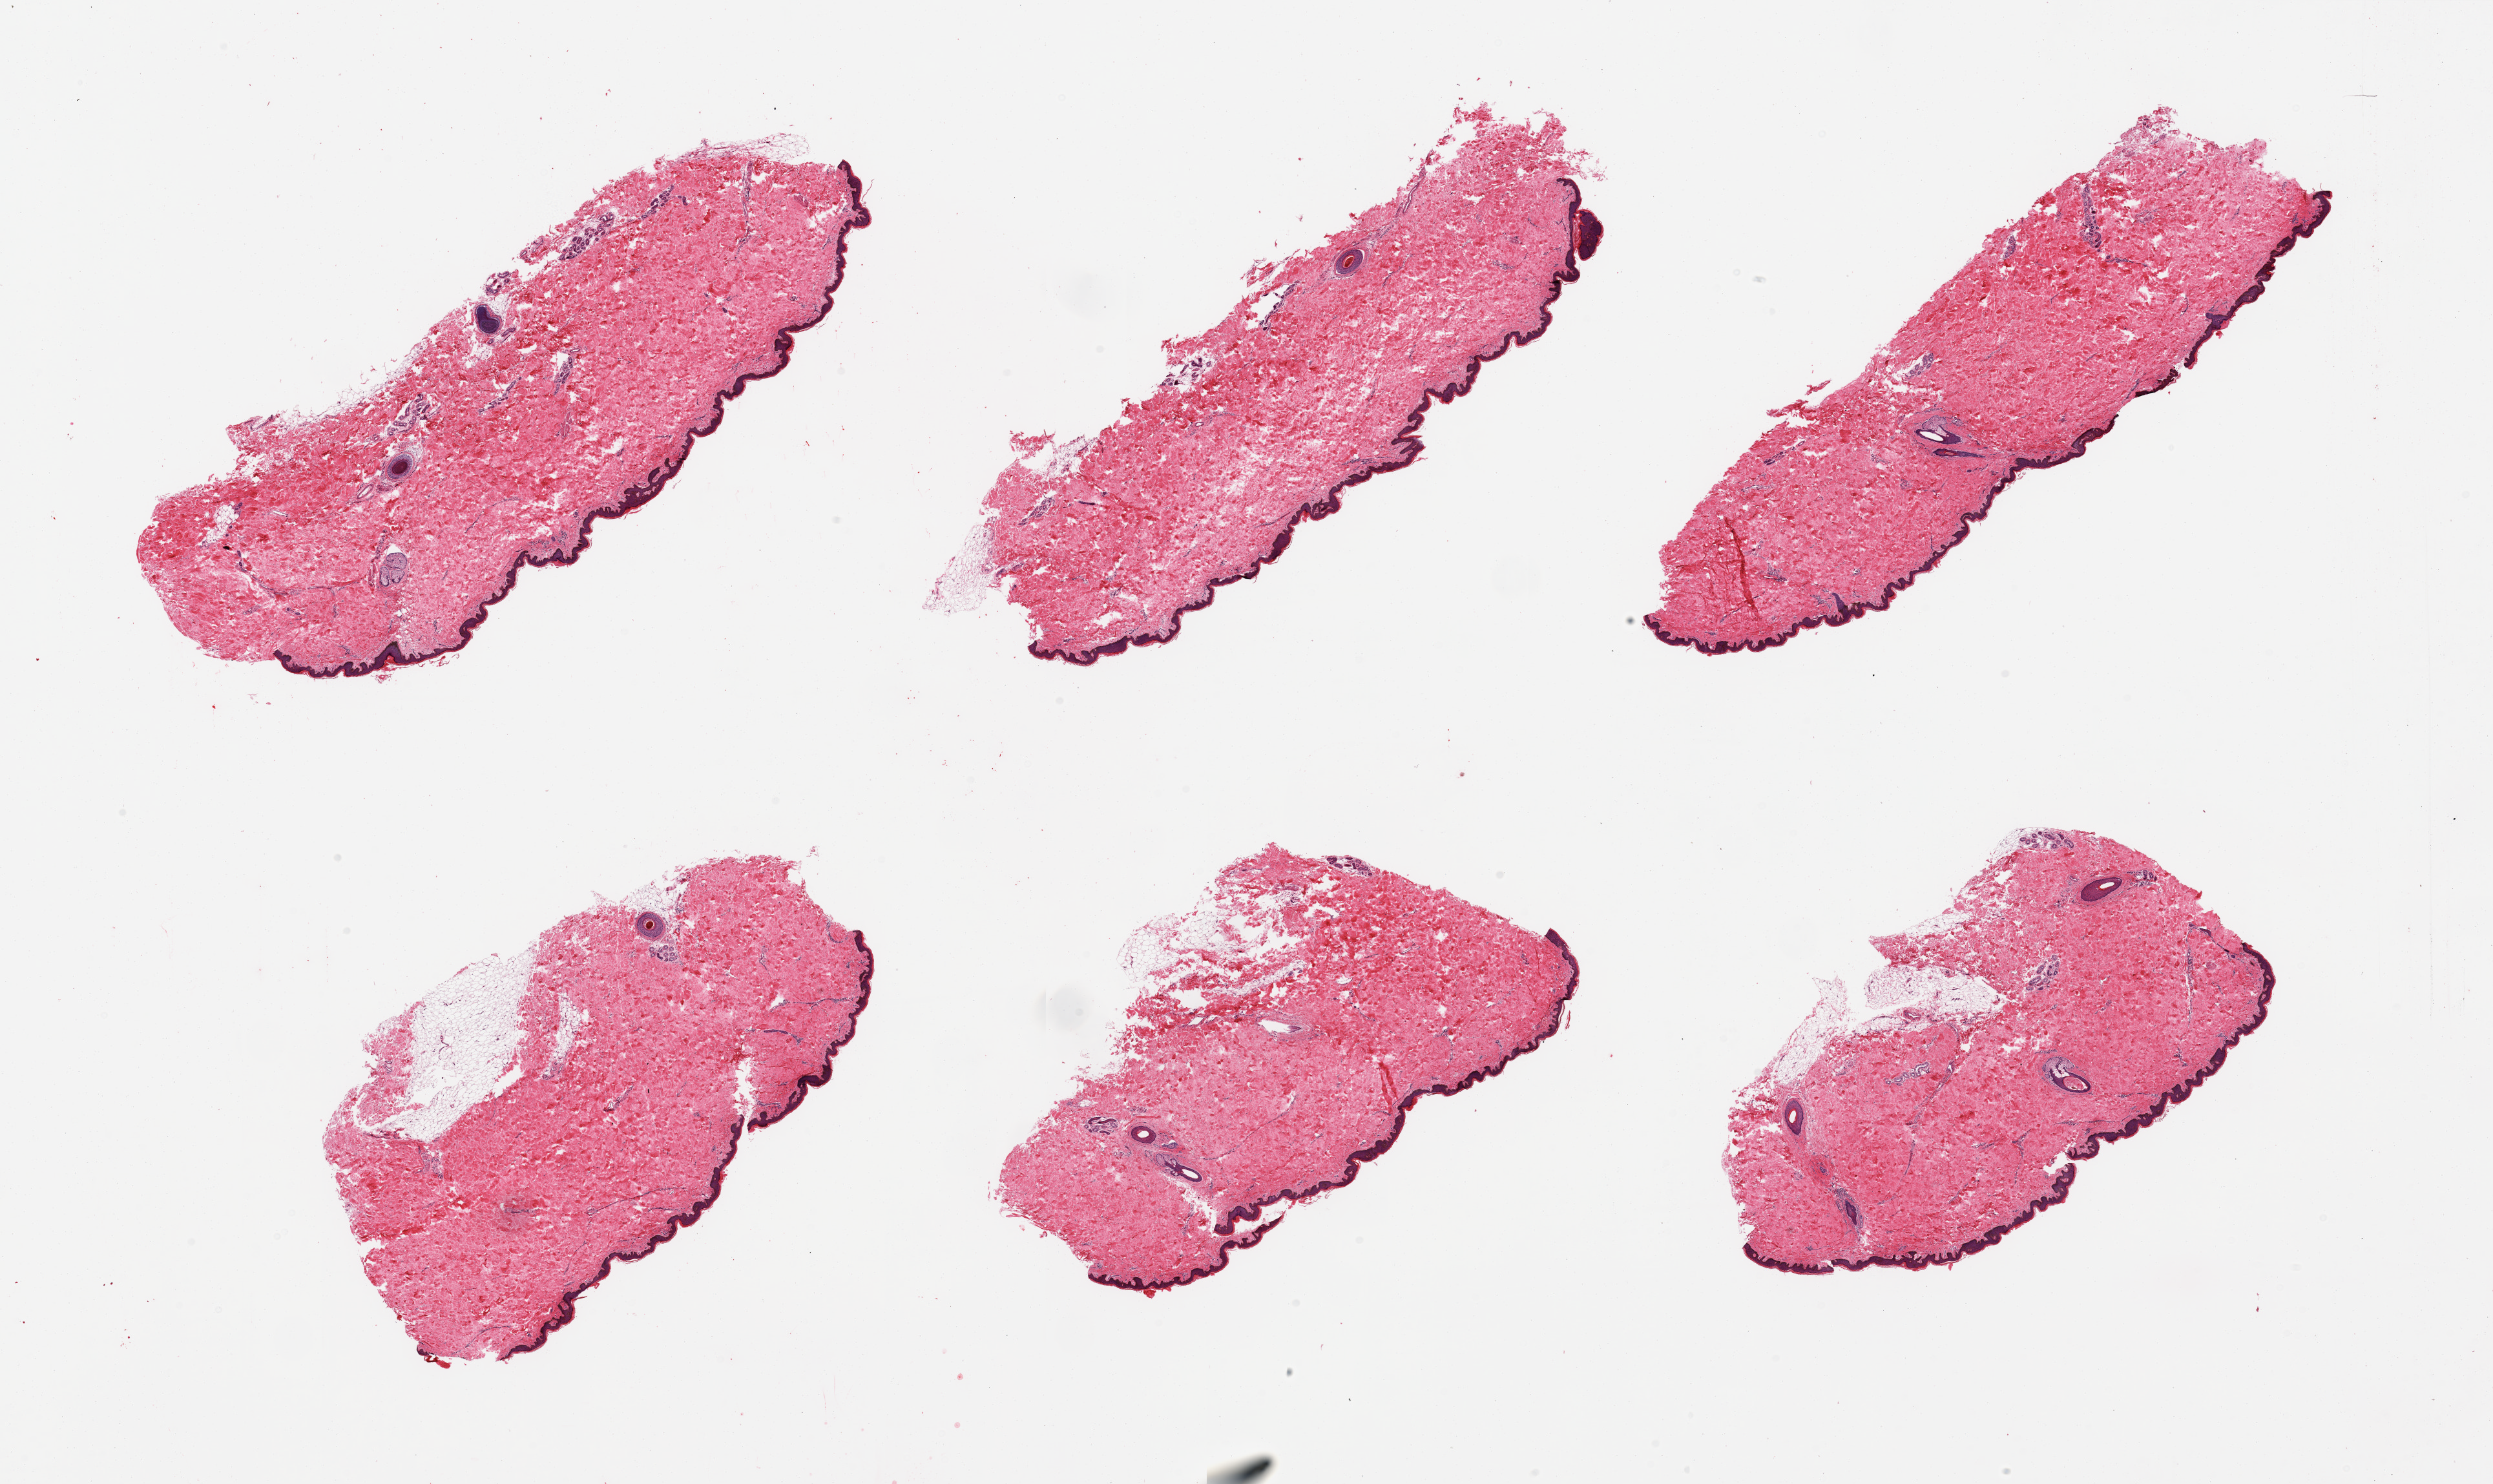
Whole-slide image, hematoxylin and eosin (H&E) stain — whole scanned area (about 30.5 x 18.2 mm) shown as a low-resolution overview. PAXgene-fixed paraffin-embedded (PFPE) section. Section of skin of suprapubic region (target tissue). Tissue donor sample. Donor sex: male.
Pathologist's review note for this sample: 6 pieces; 3 have deep pockets of fat up to 1.3mm across.